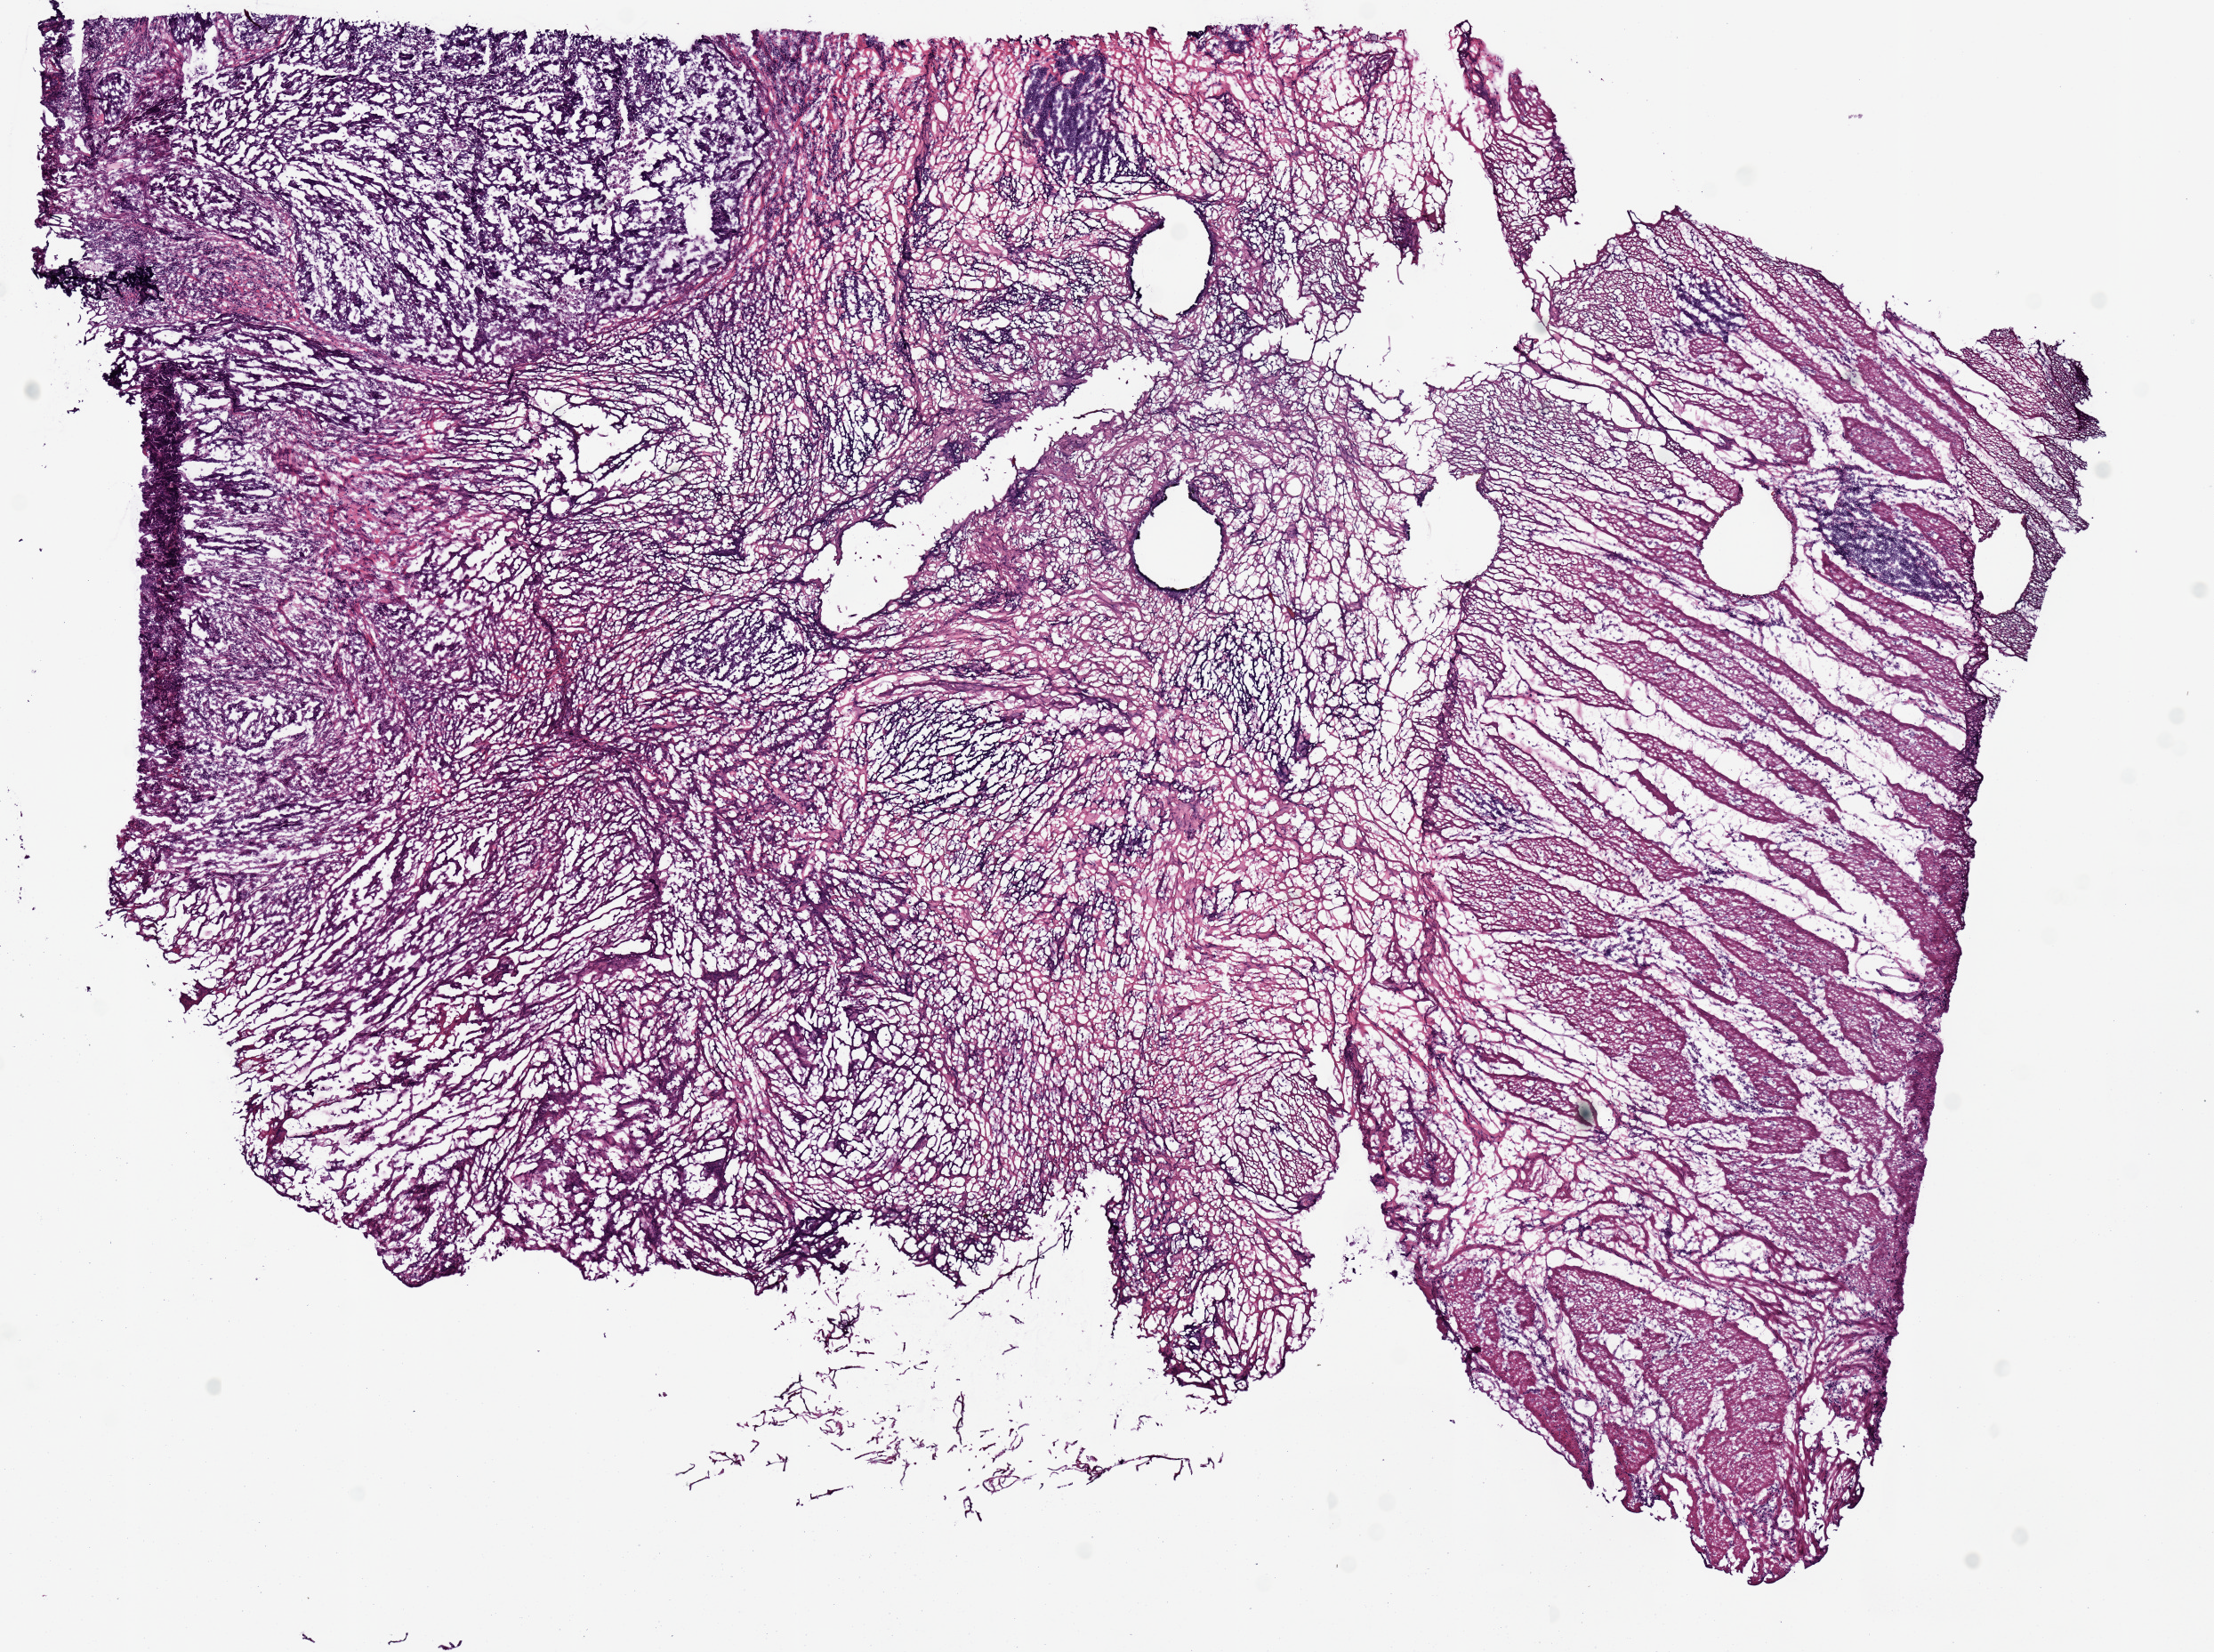
Whole-slide histology image, Hematoxylin and eosin (H&E) stained, a low-resolution overview of the entire scanned area, about 9.8 x 7.3 mm (acquisition: 20x scan), frozen section, stomach, primary tumour sample. Patient: female, age at initial diagnosis 58 years. Histologic grade: G2 (moderately differentiated). Slide review estimates, as recorded: tumour nuclei 70%, necrosis 5%.
Pathologic diagnosis: Adenocarcinoma, intestinal type (body of stomach). Lymph nodes positive (case pathology): 2 of 7 examined. AJCC pathologic stage: IIIB (7th edition).